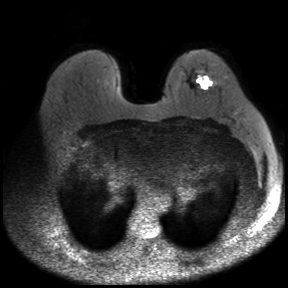
Breast MRI, one axial slice; position 24 of 30 along the scan axis; diffusion-weighted series; image 2 of 4 stored at this slice position (different b-values; order by instance number); 3 T; 288 × 288 image matrix, field of view 360 × 360 mm. Female patient.
Annotated regions visible in this slice (outlined manually by an expert reader):
- tumour on diffusion-weighted imaging: box from (x=202, y=79) to (x=211, y=88) px